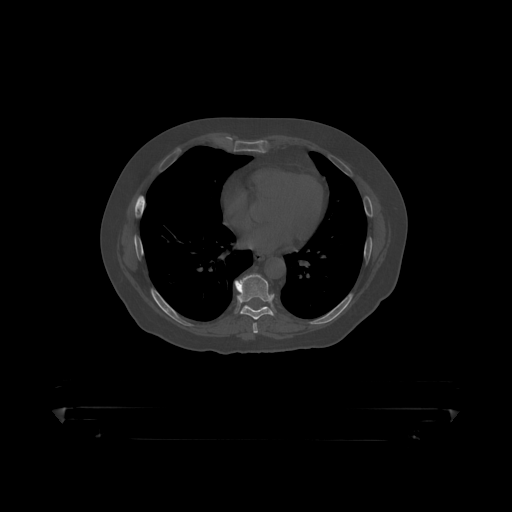
CT including the spine, one axial slice; bone window (W 1800 / L 400 HU); 512 × 512 image matrix, field of view 650 × 650 mm. Patient: male, 60 years. Case-level facts recorded for this patient, not image findings: primary cancer: prostate.
Annotated regions visible in this slice (semi-automatically segmented with operator editing):
- T8 vertebra: bounding box (x1, y1, x2, y2) in pixels: (235, 275, 275, 319)
- T9 vertebra: (244, 305, 251, 309)